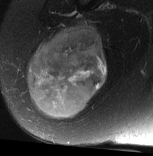
MRI of an extremity soft-tissue mass, one axial slice. Position 31 of 77 along the scan axis. T2-weighted fat-saturated. MR volume resampled by the dataset authors to the PET/CT grid (not the native acquisition matrix). 3.27 mm slice thickness. 153 × 156 image matrix. Female patient. From the clinical record (not read from this slice): histological type: synovial sarcoma; grade: intermediate; site of the primary tumour: right buttock.
Outlined on this slice (expert contour drawn on MRI and transferred to this co-registered scan by the dataset authors):
- gross tumour volume including surrounding oedema: box from (x=26, y=22) to (x=107, y=119) px
- gross tumour volume (mass): (x=26, y=26)–(x=107, y=119)